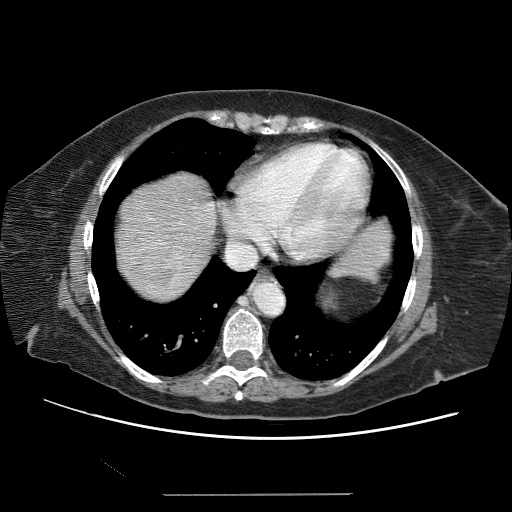
Contrast-enhanced abdominal CT (liver protocol), one axial slice; 120 kVp; soft-tissue window (W 400 / L 40 HU); 512 × 512 image matrix. From the clinical record (not read from this slice): diagnosis: hepatocellular carcinoma (patient treated with transarterial chemoembolisation; whether this scan precedes or follows treatment is not stated here); TNM stage (as recorded): Stage-IIIB; Child-Pugh class: A; tumour nodularity: uninodular.
Annotated regions visible in this slice (semi-automatic segmentation, software-assisted and operator-edited):
- abdominal aorta: bounding box <256,284,285,317> (left, top, right, bottom; pixels)
- liver parenchyma outside the tumour (the mass and vessels are separate outlines, so this box may not span the whole liver): <124,178,214,278>
- mass: <125,232,193,293>
- liver vessels: <163,197,212,255>